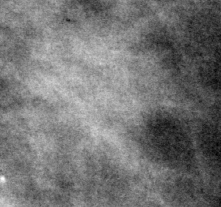
Region of interest cut from a scanned film mammogram (one marked finding), left breast, MLO view.
Finding: mass, shape irregular, margins spiculated; BI-RADS assessment category 4; subtlety rating 3 on a 1 (subtle) to 5 (obvious) scale; pathology result (as recorded, not read from the image): malignant.